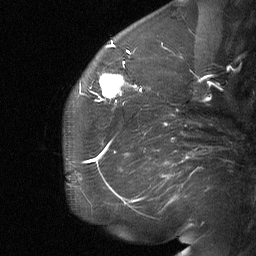
Breast MRI (dynamic contrast-enhanced), one sagittal slice; slice 21 of 64 in the series (ordered by position); dynamic contrast-enhanced study with each time point stored as its own series, time point 2 of 3 at this slice position (early post-contrast, ordered by acquisition time); 1.5 T; TE 4.8 ms, TR 27 ms; 2 mm slice thickness; 256 × 256 image matrix, field of view 200 × 200 mm. Patient: female, 60 years. Case-level facts recorded for this patient, not image findings: setting: breast cancer imaged before/during neoadjuvant chemotherapy; receptor status: HR-positive, HER2-negative.
Outlined on this slice (semi-automatic segmentation, software-assisted and operator-edited):
- analysis volume of interest (the breast-tissue region the enhancement analysis was run in; not a lesion): bounding box [x1, y1, x2, y2] px = [91, 56, 139, 104]
- tumour enhancement mask (voxels above the 90 % enhancement threshold inside the analysis volume of interest): [99, 73, 137, 100]